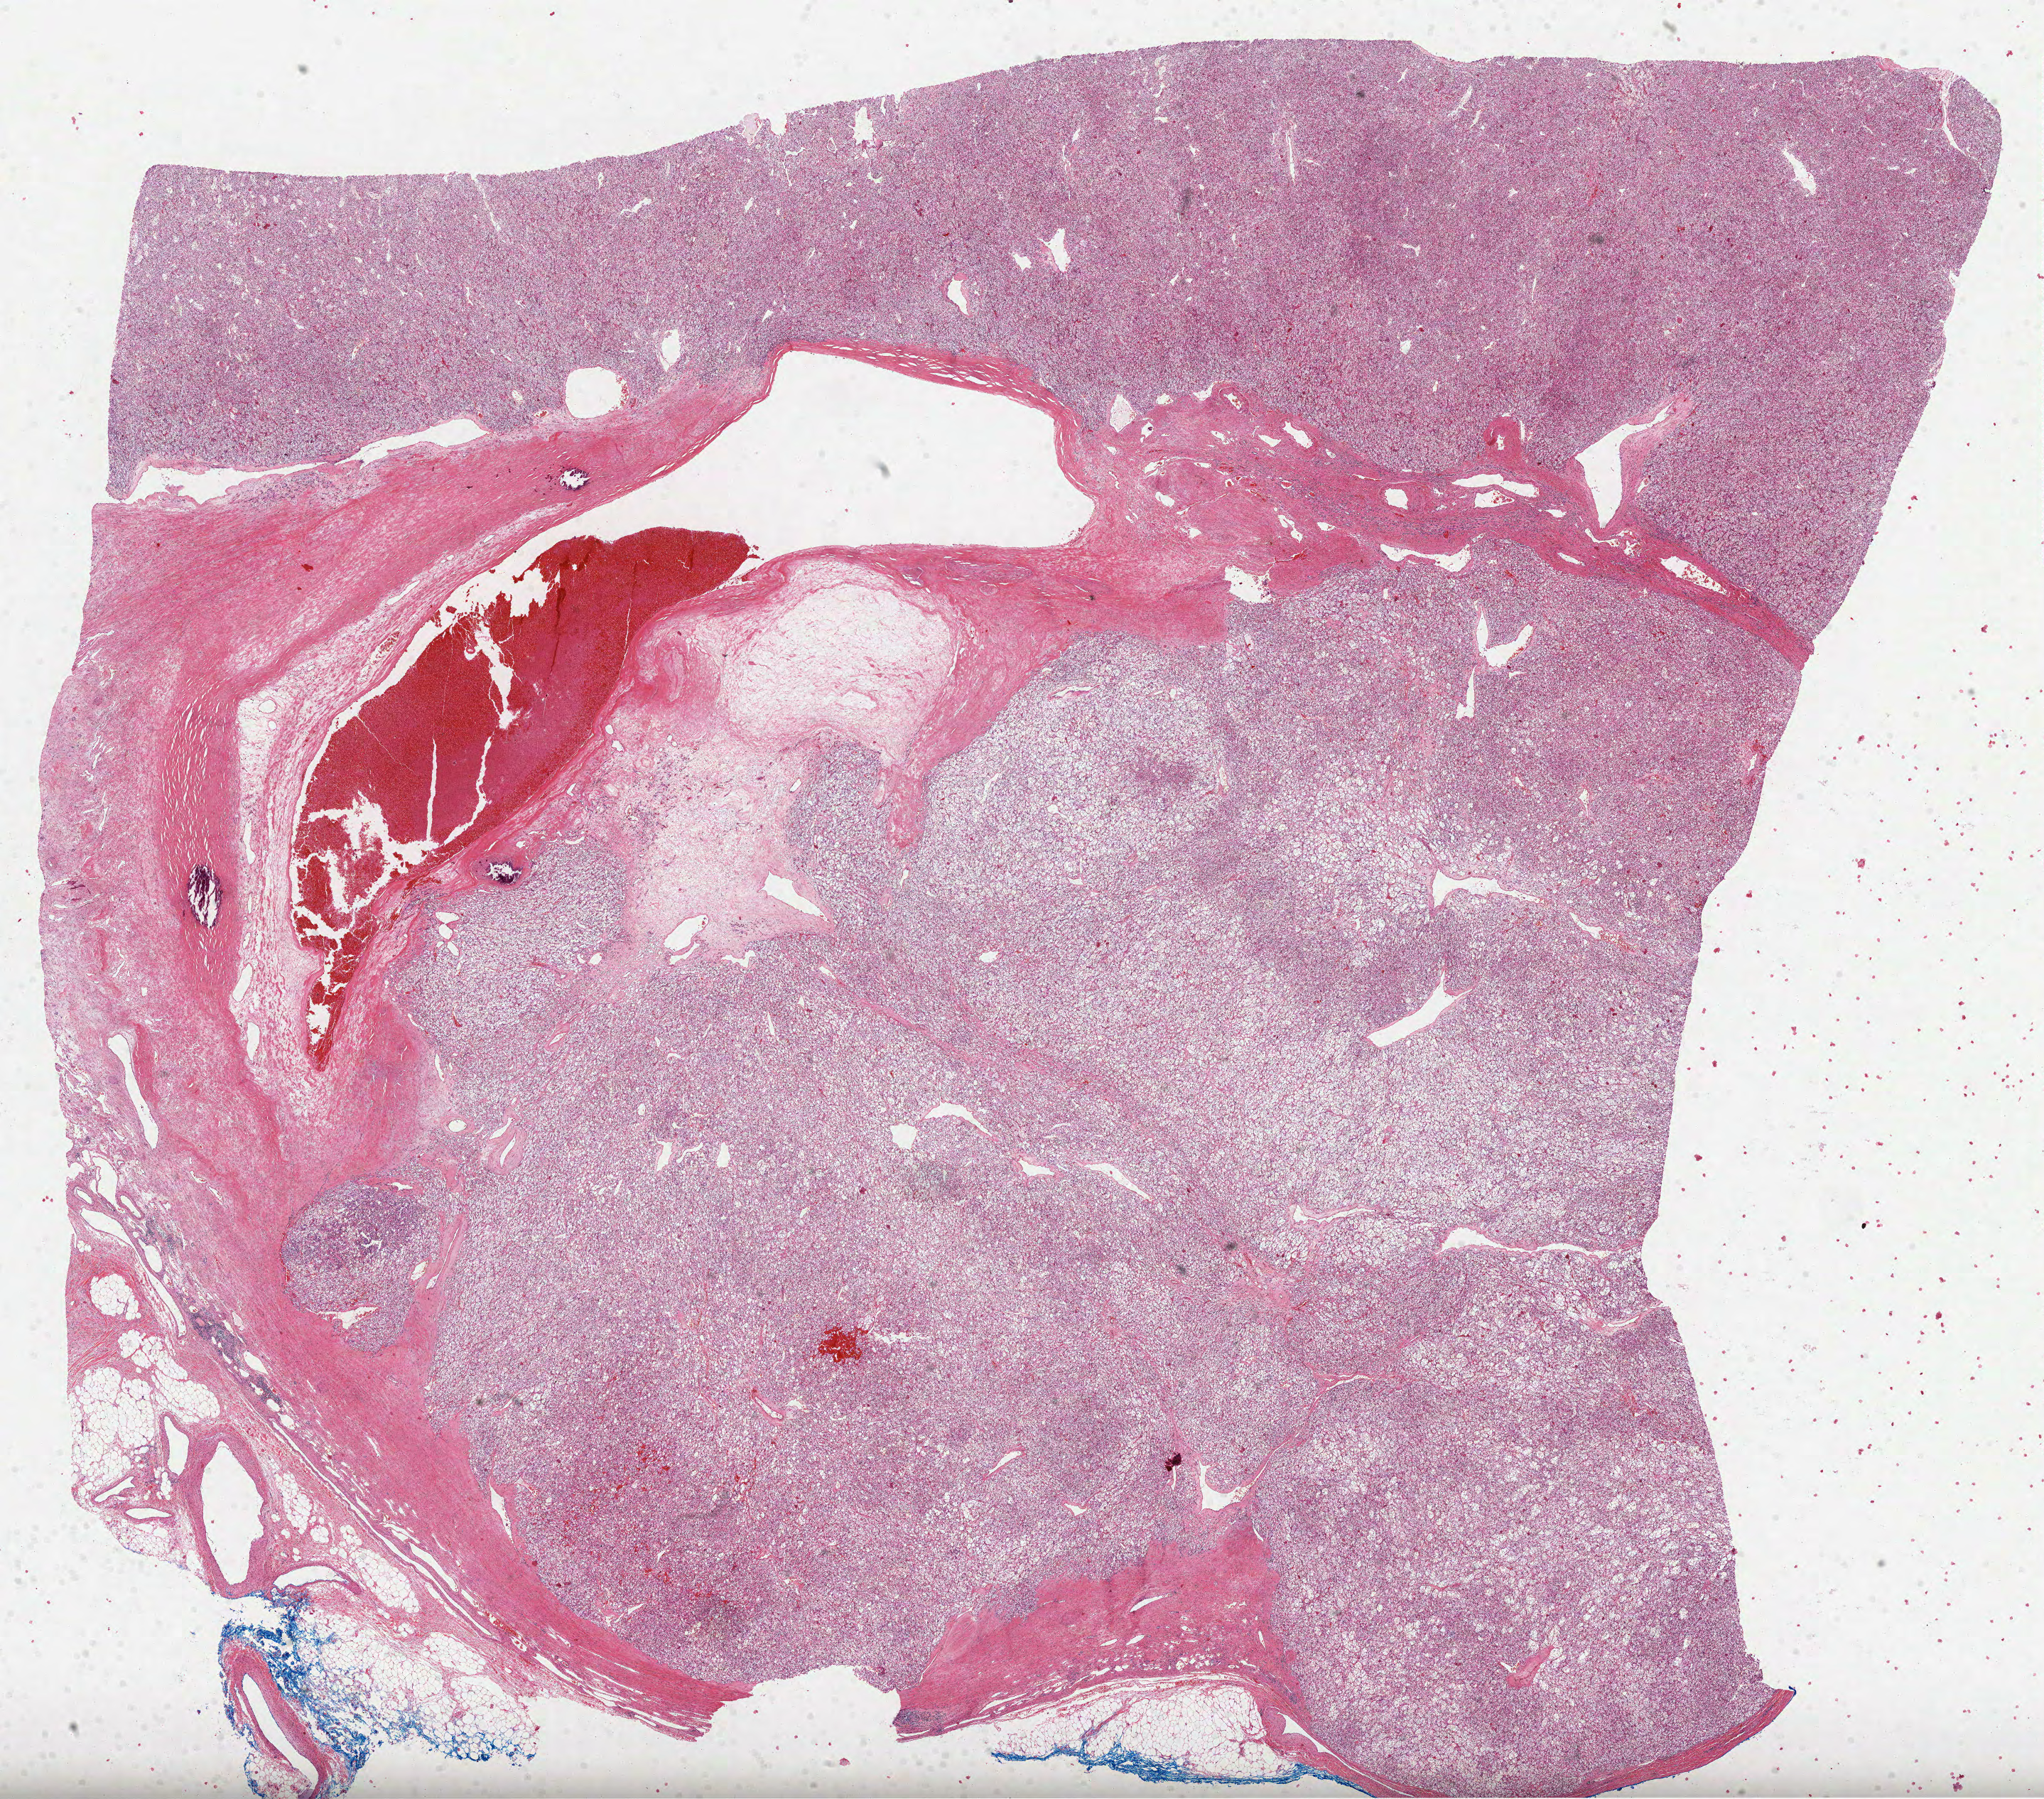
Whole-slide histology image, Hematoxylin and eosin (H&E) stained — whole scanned area (about 23.2 x 20.4 mm, acquisition: 40x scan) shown as a low-resolution overview, FFPE section, kidney, primary tumour sample. Male, age 61 years at initial diagnosis. Histologic grade: G4 (undifferentiated).
Laterality: left. Diagnosis: Clear cell adenocarcinoma, NOS. TNM: T3a NX M0. AJCC pathologic stage: III.